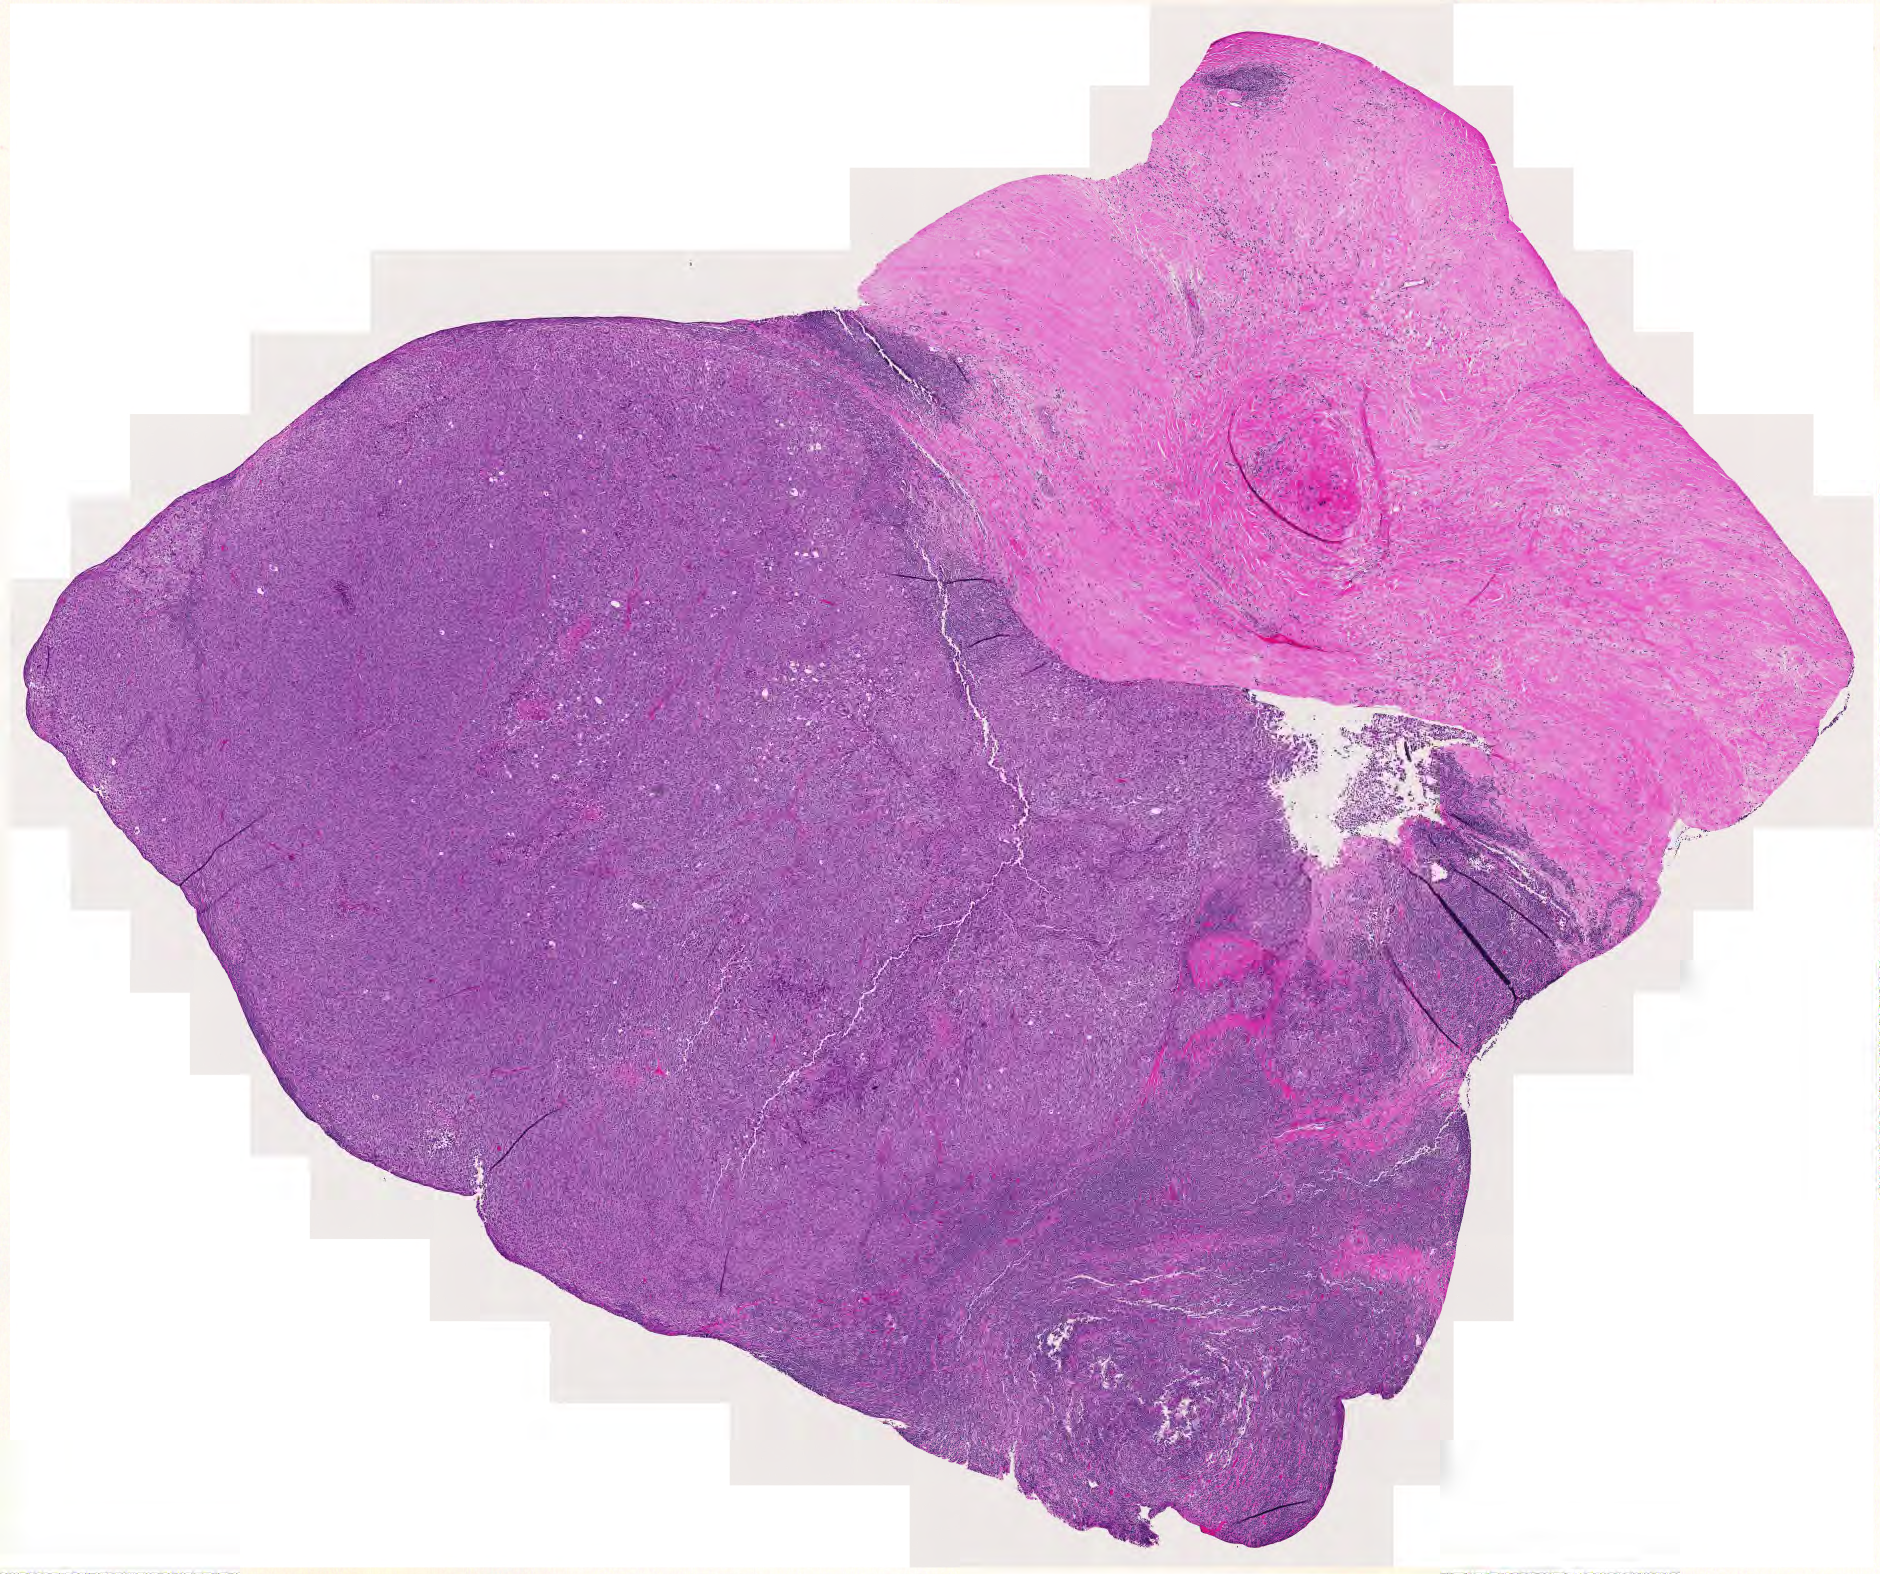
H&E whole-slide image — whole scanned area (about 9.7 x 8.1 mm, acquisition: 20x scan) shown as a low-resolution overview; melanoma tumour tissue; sampled site not recorded. 68-year-old male patient.
Diagnosis: Malignant melanoma, NOS. AJCC pathologic stage: 0.